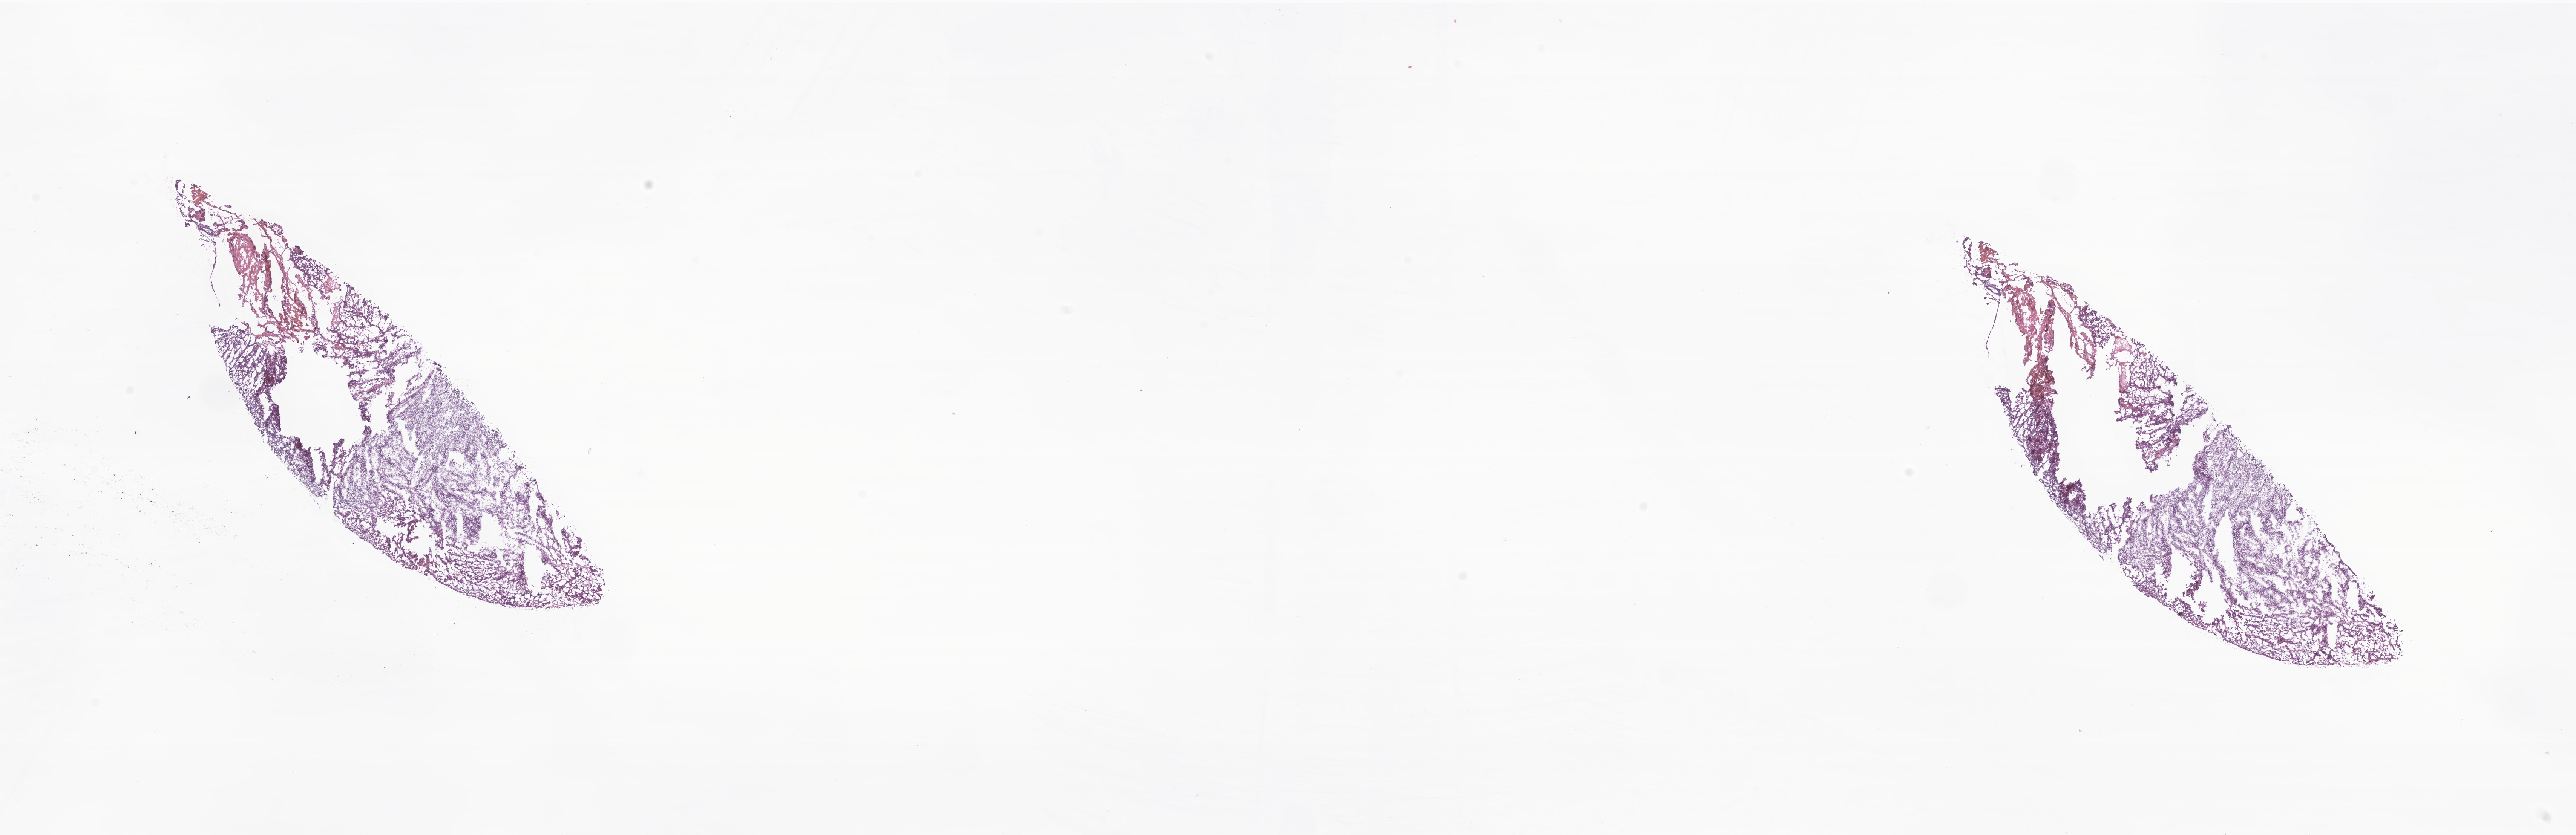
Whole-slide image, H&E stain of tumor tissue from the cerebellum — low-resolution overview of the scanned area, about 28.8 x 9.3 mm; frozen section. Patient male; age 132 months (11 years).
• diagnosis: Medulloblastoma, NOS